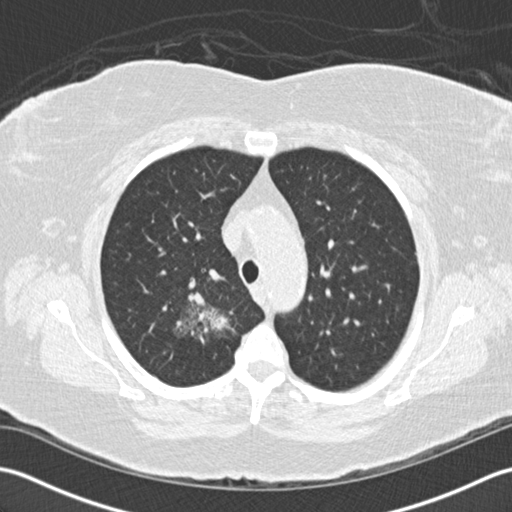
Axial slice from a low-dose chest CT screening exam. Baseline screening round. Lung window (W 1500 / L -600 HU). 2 mm slice thickness. Standard (soft-tissue) reconstruction kernel (B30f). 120 kVp. Slice 35 of 156 in the series. 512 × 512 image matrix, field of view 350 × 350 mm. Female participant, aged 72 years at enrolment. Former smoker at enrolment.
- Lesion marked by an expert reader, bounding box <139,273,239,368> (left, top, right, bottom; pixels).
- The screening reader recorded 2 non-calcified nodules or masses ≥4 mm on this exam; which of them this box marks is not recorded.
- Later outcome: lung cancer diagnosed 494 days after this screen — bronchiolo-alveolar adenocarcinoma, NOS, right upper lobe, stage IIIB (AJCC 6th edition), 45 mm at pathology.